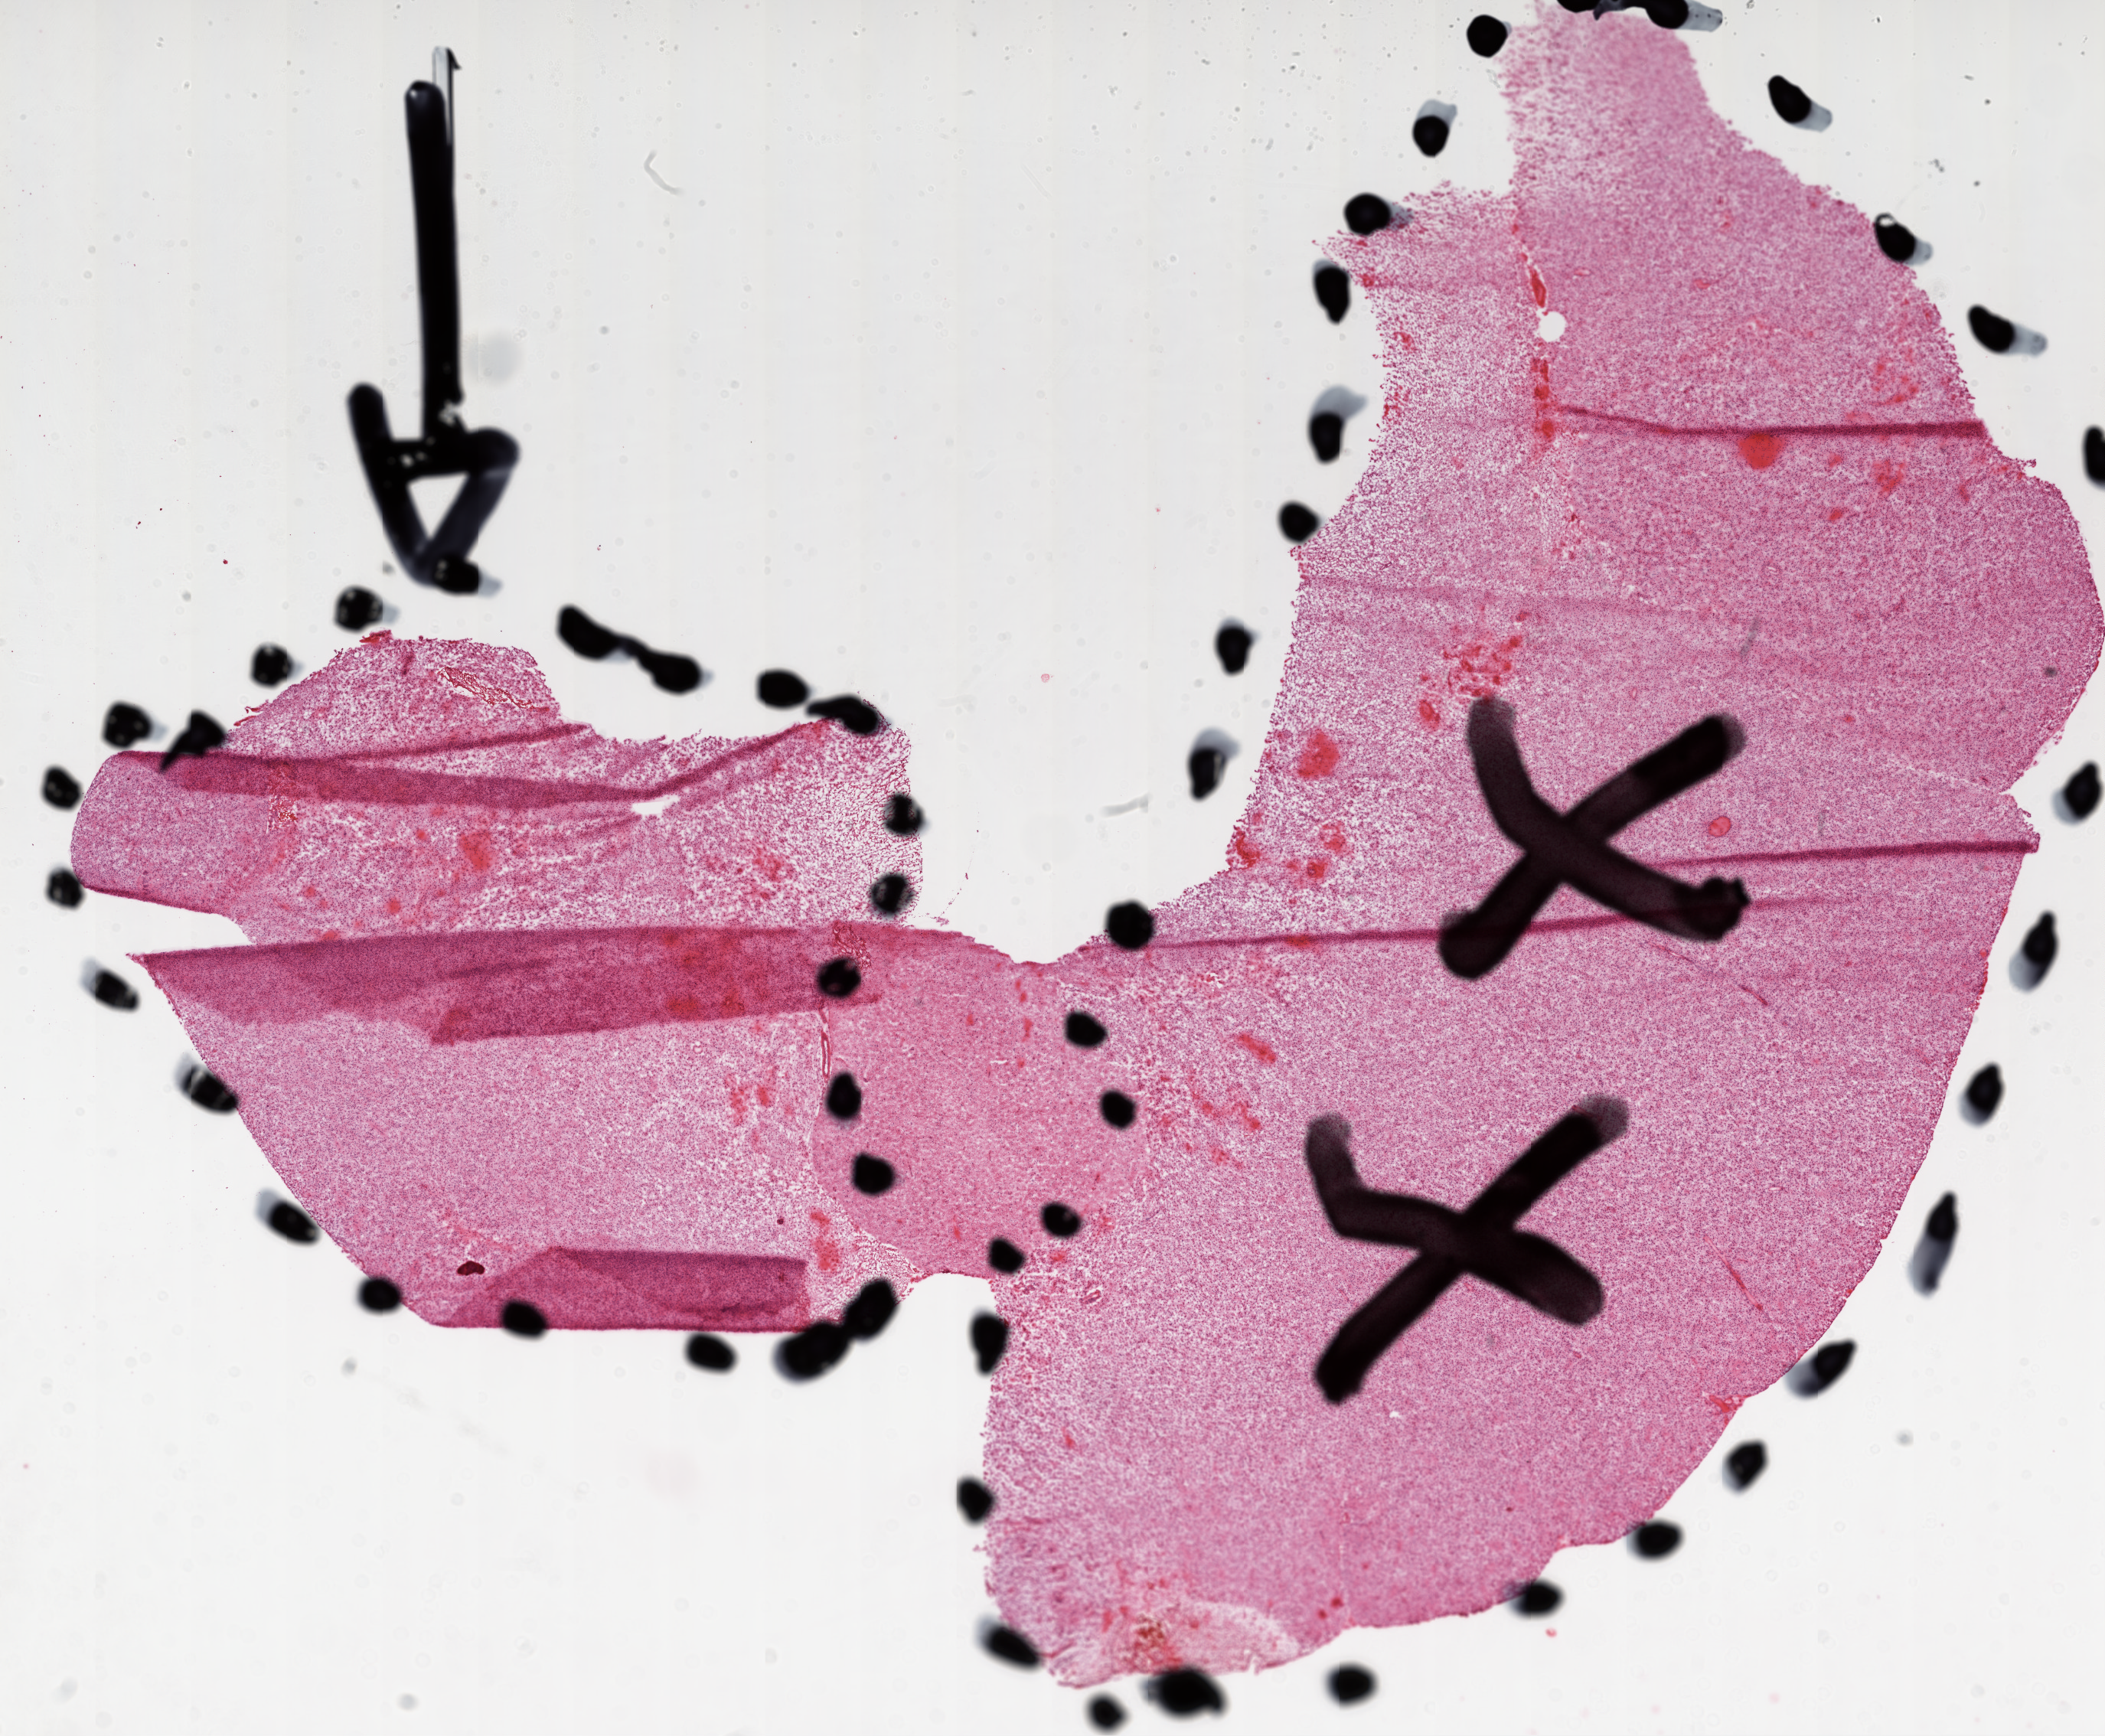
Whole-slide histology image, Hematoxylin and eosin (H&E) stained — whole scanned area (about 22.1 x 18.2 mm, acquisition: 20x scan) shown as a low-resolution overview; frozen section; primary tumour sample from the brain. Patient: male, age at initial diagnosis 55 years. Pathologist review of this section (percent, as recorded): tumour cells 95%, tumour nuclei 95%, normal cells 5%, stromal cells 0%, necrosis 0%.
• pathologic diagnosis: Glioblastoma